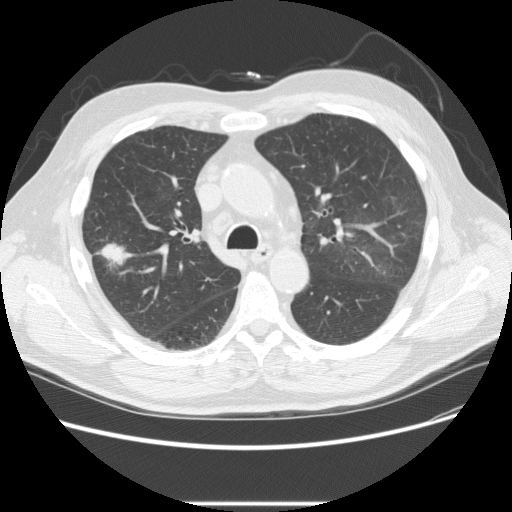
Low-dose screening chest CT, one axial slice; slice 155 of 233 in the series (ordered by position); reconstruction kernel STANDARD; lung window (W 1500 / L -600 HU); 2.5 mm slice thickness; 512 × 512 image matrix, field of view 380 × 380 mm.
Outlined on this slice (outlined manually by an expert reader):
- lesion 2 (tumor, upper lobe of right lung): bounding box <98,242,130,267> (left, top, right, bottom; pixels)